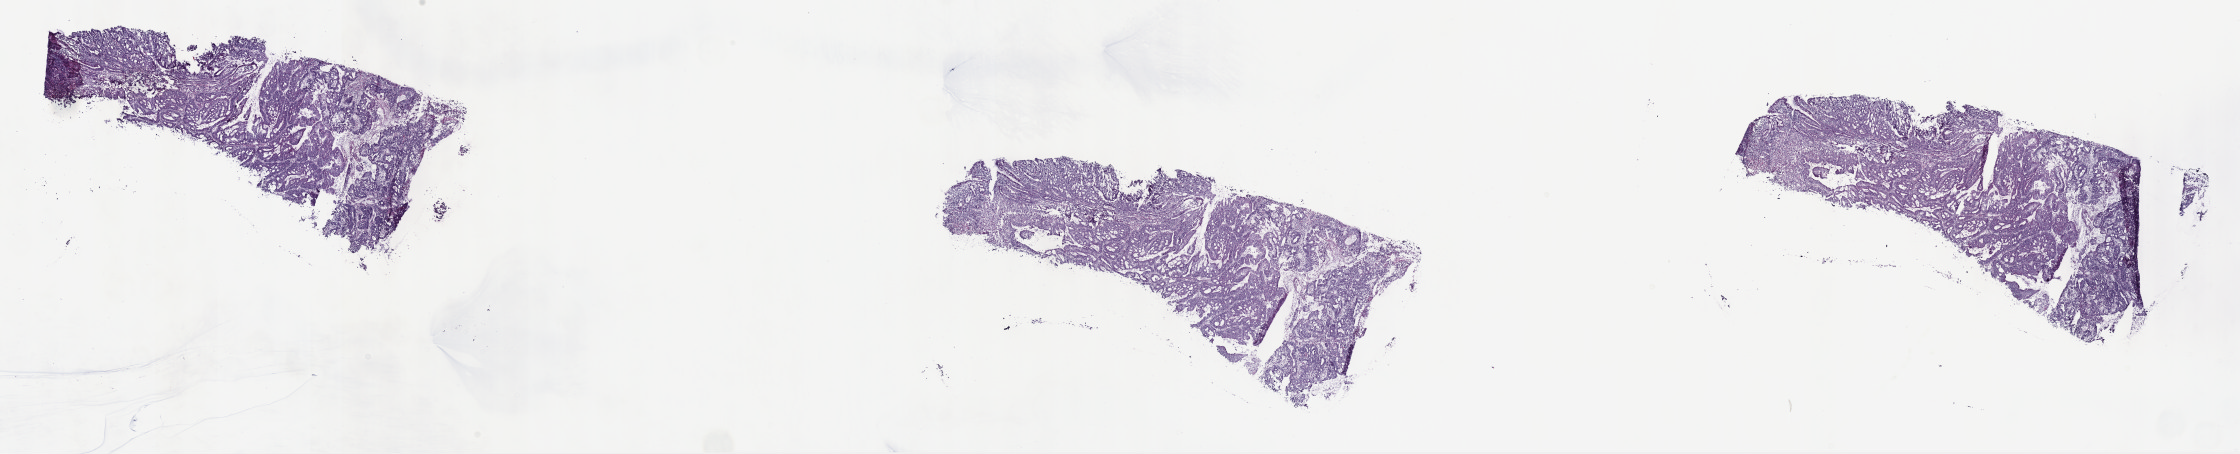
Whole-slide histology image, Hematoxylin and eosin (H&E) stained — shown as a low-resolution overview of the whole scanned area (about 36.2 x 7.3 mm, slide scanned at 40x), frozen section from the top of the tissue portion, sample: primary tumour, stomach. Patient: female, age at initial diagnosis 67 years. Histologic grade: G3 (poorly differentiated). Composition of this section per pathologist review: tumour cells 70%, tumour nuclei 70%, normal cells 0%, stromal cells 25%, necrosis 5%. Infiltration values recorded for this section: lymphocyte infiltration 40%, monocyte infiltration 20%, neutrophil infiltration 20%.
* pathologic diagnosis: Adenocarcinoma, intestinal type (gastric antrum)
* AJCC pathologic stage: IIIB (7th edition)
* TNM: T4b N0 M0
* lymph nodes positive (case pathology): 0 of 29 examined